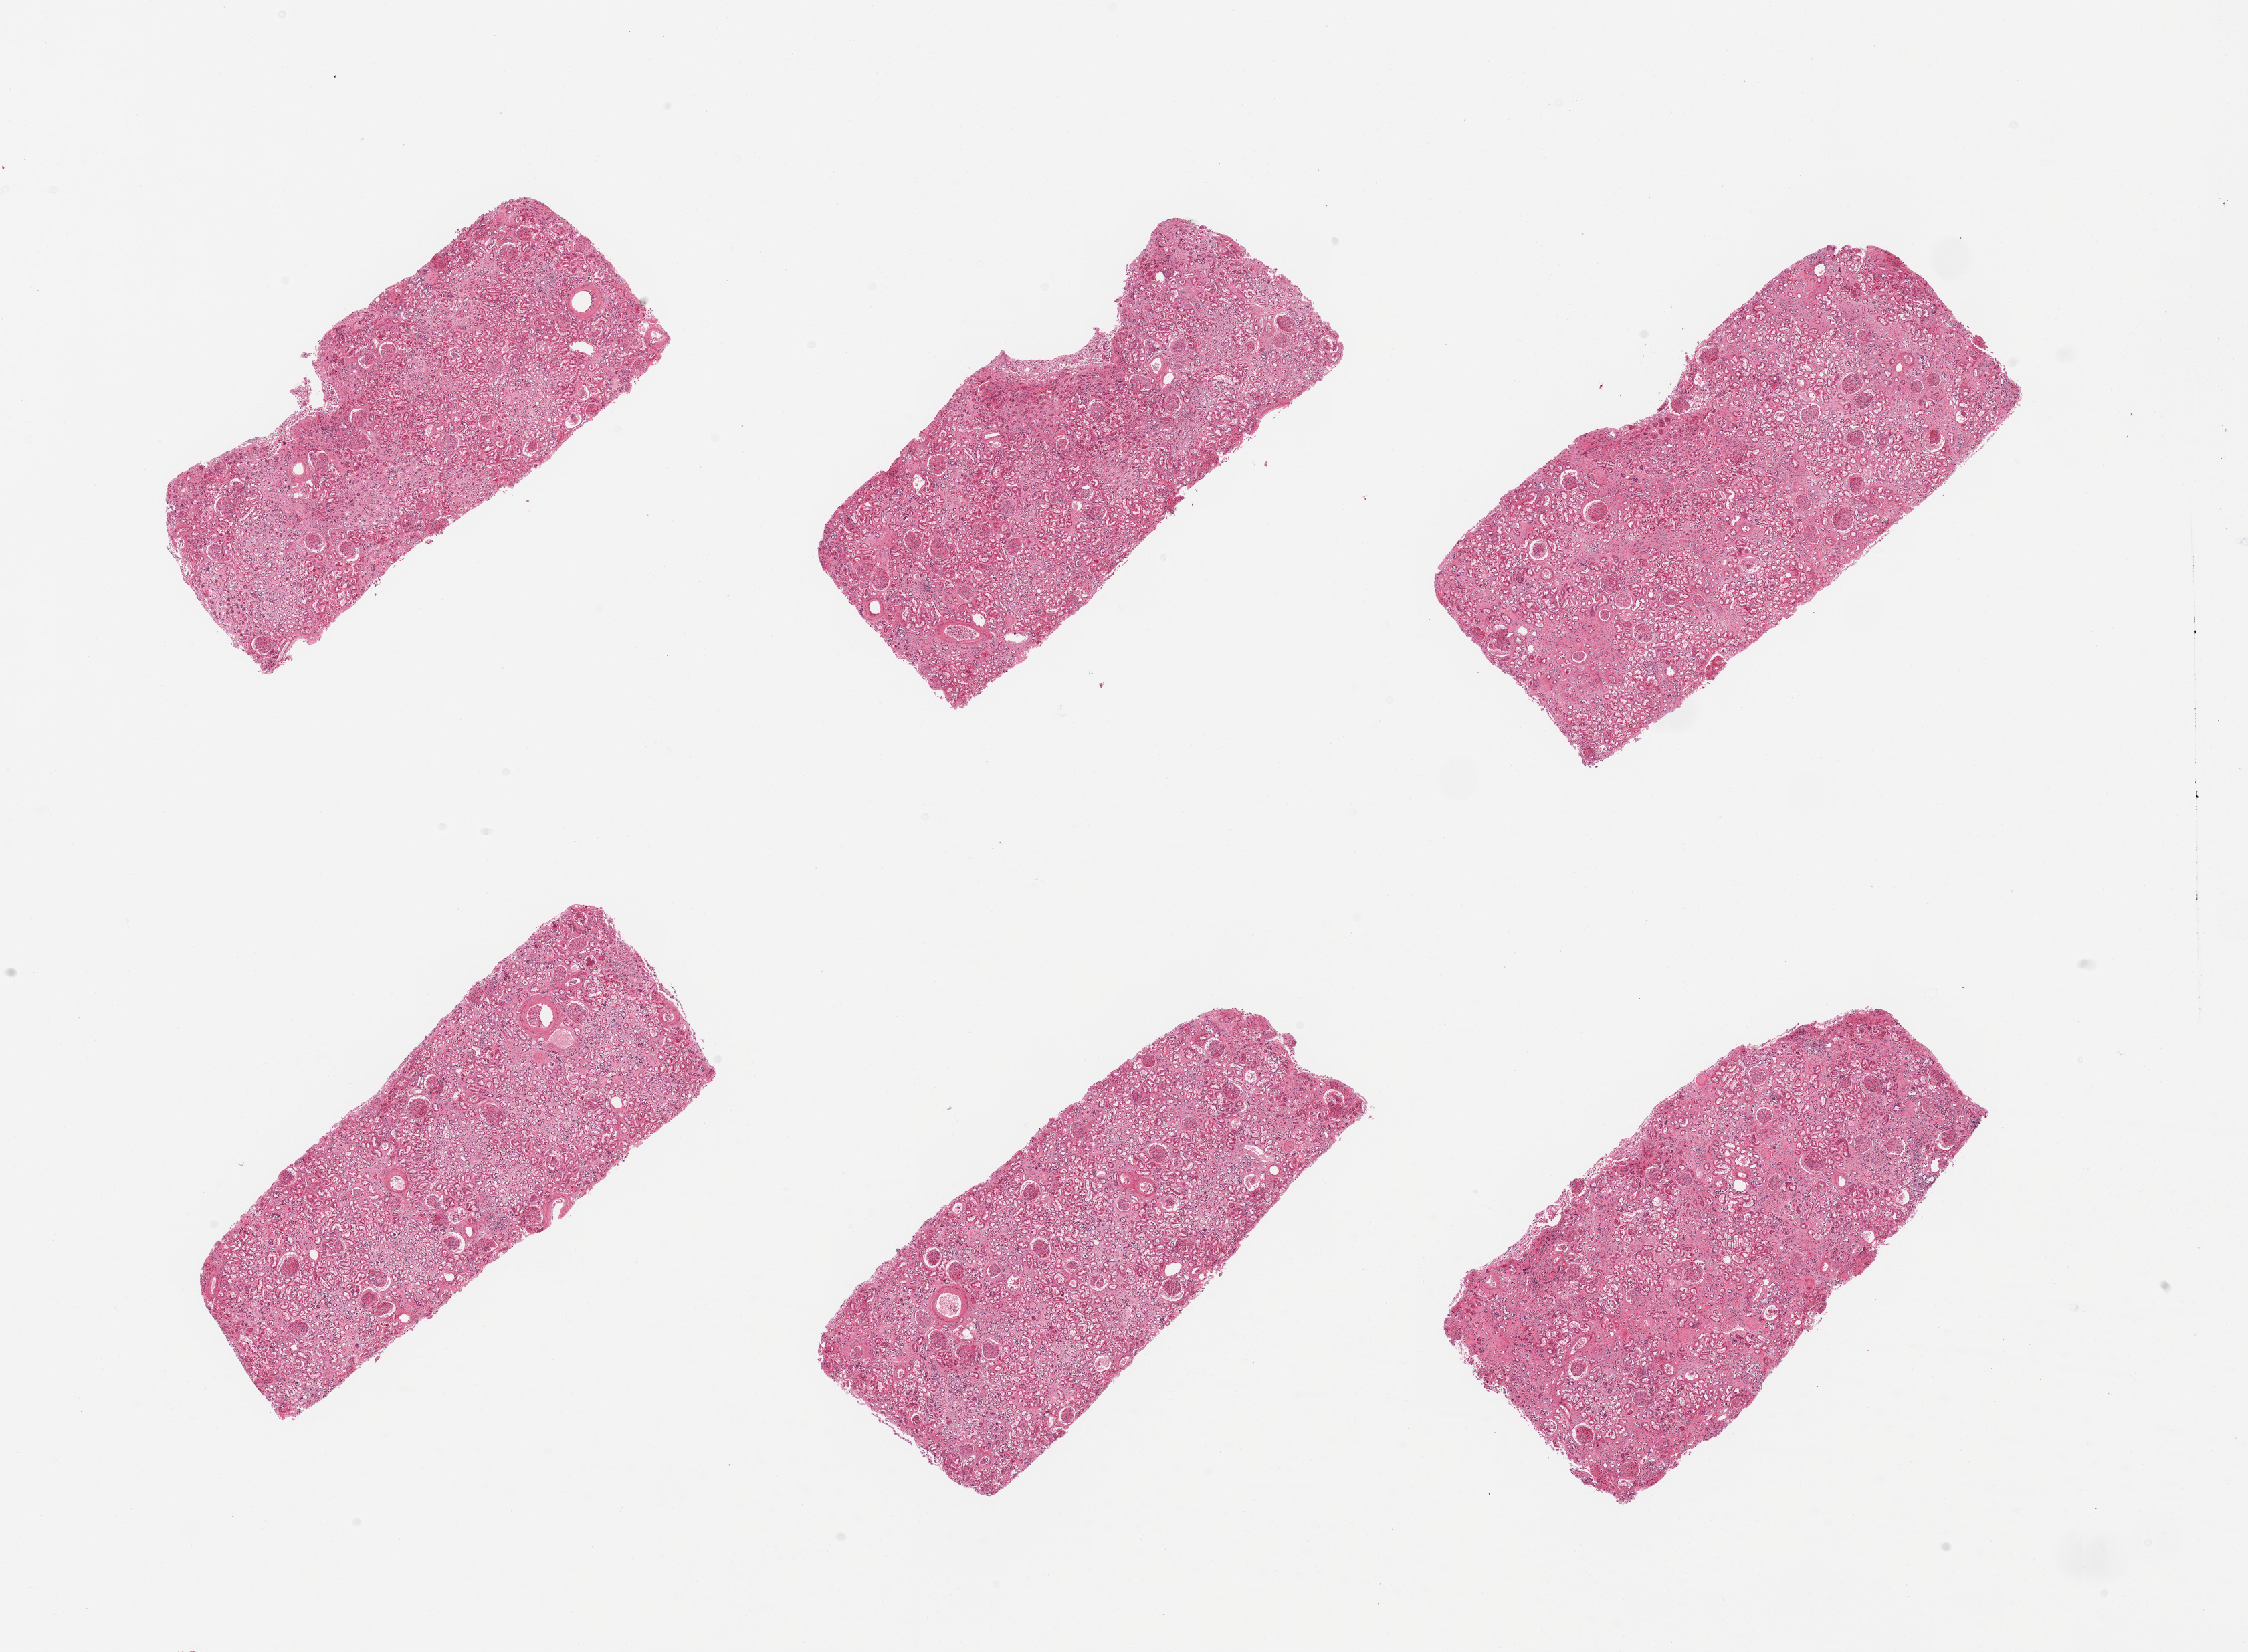
H&E whole-slide image, low-resolution overview of the scanned area, about 26.6 x 19.5 mm (from a 20x scan); PAXgene-fixed paraffin-embedded (PFPE) section; section of renal cortex (target tissue); tissue donor sample. Donor: male.
Pathologist's review note for this sample: 6 pieces; arterio and arteriolonephrosclerosis, scattered hyalinized glomeruli (representative findings).